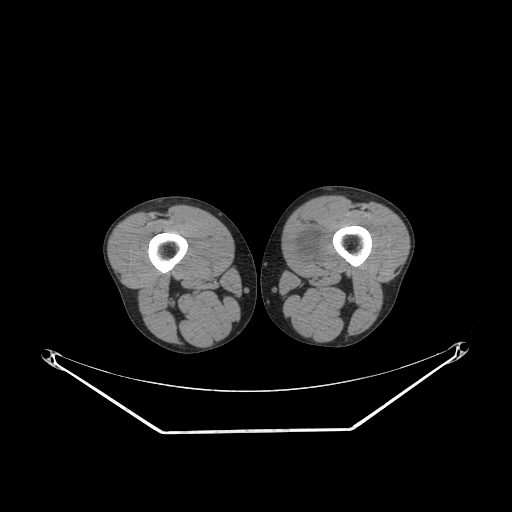
CT of an extremity soft-tissue mass (from a PET/CT study), one axial slice; slice 230 of 311 in the series (ordered by position); 140 kVp; soft-tissue window (W 400 / L 40 HU); 3.75 mm slice thickness; 512 × 512 image matrix, field of view 500 × 500 mm. Male patient. From the clinical record (not read from this slice): histological type: mixoid liposarcoma; grade: low; site of the primary tumour: left thigh.
Annotated regions visible in this slice (expert contour drawn on MRI and transferred to this co-registered scan by the dataset authors):
- gross tumour volume (mass): box from (x=288, y=228) to (x=323, y=266) px